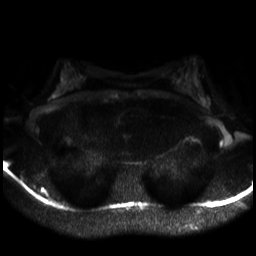
Breast MRI, one axial slice; position 17 of 30 along the scan axis; diffusion-weighted series; image 2 of 4 stored at this slice position (different b-values; order by instance number); 3 T; 4 mm slice thickness; 256 × 256 image matrix, field of view 320 × 320 mm. Female patient.
Annotated regions visible in this slice (outlined manually by an expert reader):
- tumour on diffusion-weighted imaging: bounding box <201,97,204,101> (left, top, right, bottom; pixels)